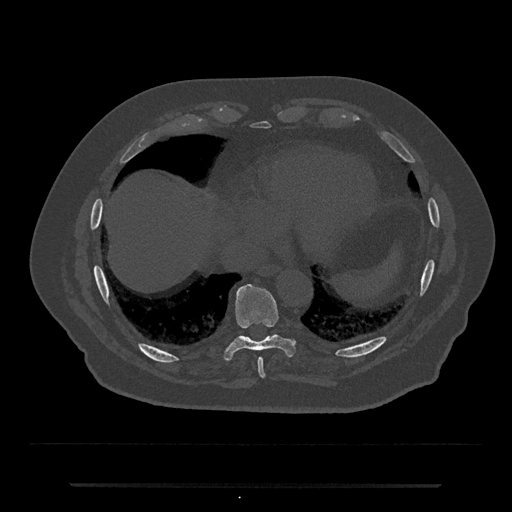
CT including the spine, one axial slice. Slice 758 of 797 in the series (ordered by position). Reconstruction kernel Br40s/3. Bone window (W 1800 / L 400 HU). 512 × 512 image matrix, field of view 434 × 434 mm. Male patient, age 80 years. Case-level facts recorded for this patient, not image findings: primary cancer: prostate; vertebrae with lytic lesions (as recorded): L1, T11.
Annotated regions visible in this slice (semi-automatic segmentation, software-assisted and operator-edited):
- T8 vertebra: box from (x=257, y=358) to (x=265, y=378) px
- T9 vertebra: (x=225, y=283)–(x=295, y=360)